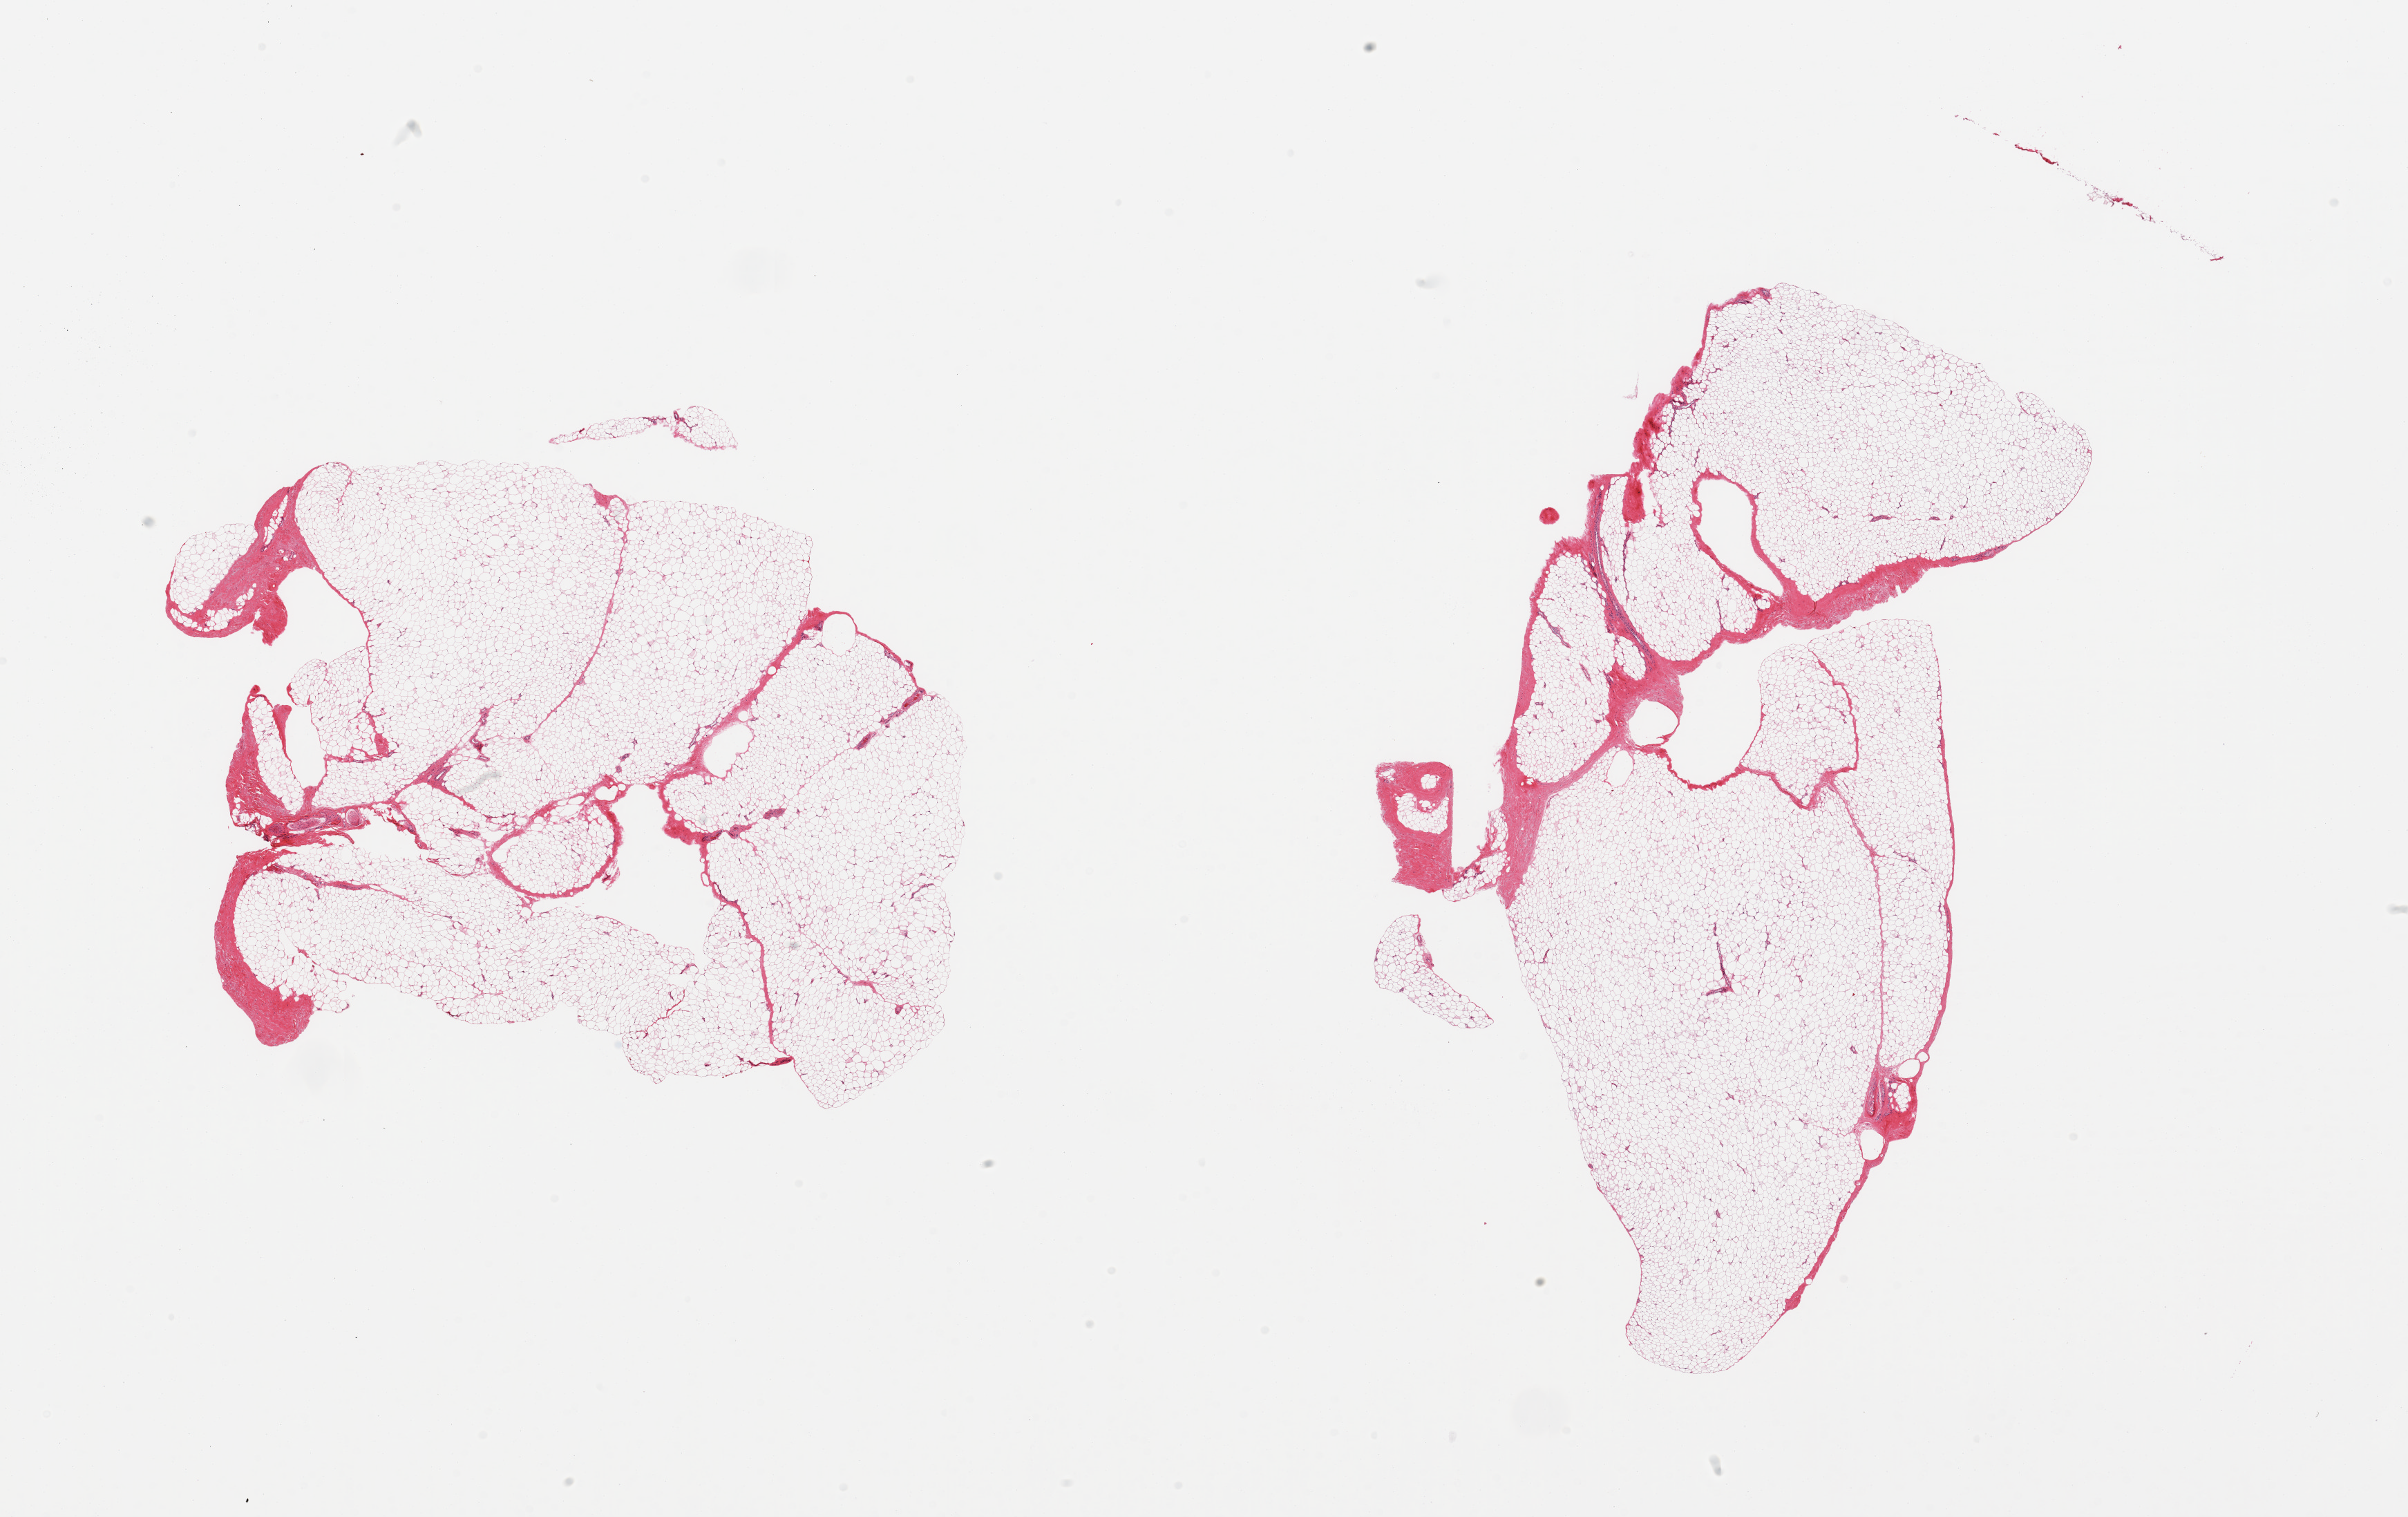
Whole-slide image, haematoxylin and eosin stain, brightfield, a low-resolution overview of the entire scanned area, about 27.6 x 17.4 mm. PAXgene-fixed, paraffin-embedded tissue. Section of adipose tissue (target tissue). Tissue donor sample.
Reviewer comment on this tissue sample: 2 pieces; fat with <10% fibrous component.